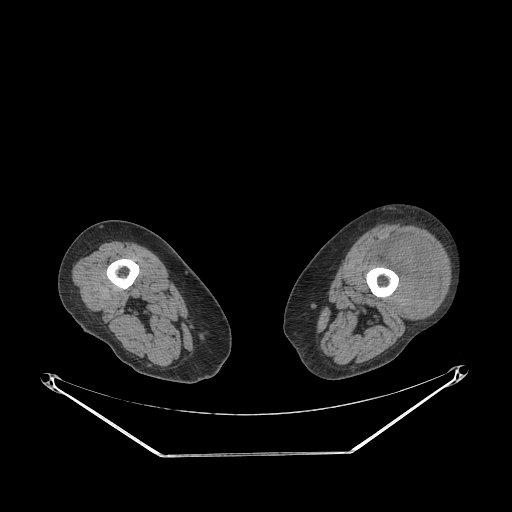
CT of an extremity soft-tissue mass (from a PET/CT study), one axial slice; slice 206 of 267 in the series (ordered by position); soft-tissue window (W 400 / L 40 HU); 3.75 mm slice thickness; 512 × 512 image matrix, field of view 500 × 500 mm. Female patient. From the clinical record (not read from this slice): histological type: undifferentiated – high grade; grade: high; site of the primary tumour: left thigh.
Annotated regions visible in this slice (expert contour drawn on MRI and transferred to this co-registered scan by the dataset authors):
- gross tumour volume including surrounding oedema: box from (x=368, y=237) to (x=439, y=318) px
- gross tumour volume (mass): (x=390, y=239)–(x=439, y=318)